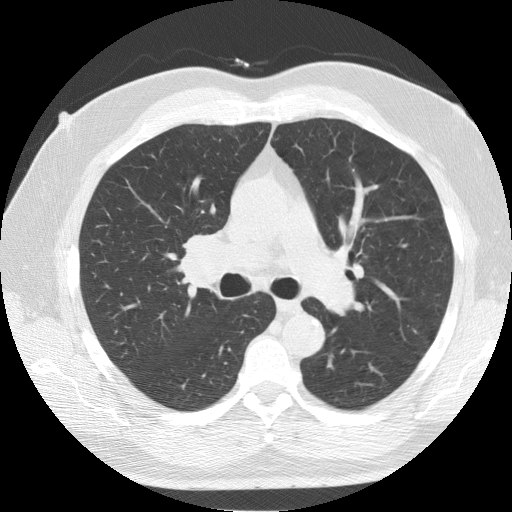
Axial slice from a low-dose chest CT screening exam, second annual screen, lung window (W 1500 / L -600 HU), 2.5 mm slice thickness, standard (soft-tissue) reconstruction kernel (STANDARD), 512 × 512 image matrix, field of view 376 × 376 mm. Male participant, aged 64 years at enrolment. Former smoker at enrolment.
Lesion marked by an expert reader, box from (x=167, y=222) to (x=258, y=302) px. Reader record for this screening exam (exam-level; its link to the box is not recorded): non-calcified nodule or mass ≥4 mm, right lower lobe, 7 × 5 mm, smooth margins, soft tissue attenuation, pre-existing on the prior screen: yes; interval growth: no. Official screen result: positive, other. Lung cancer was diagnosed 63 days after this screen: adenocarcinoma, NOS, right upper lobe, poorly differentiated (G3), stage IB (AJCC 6th edition), 37 mm at pathology.